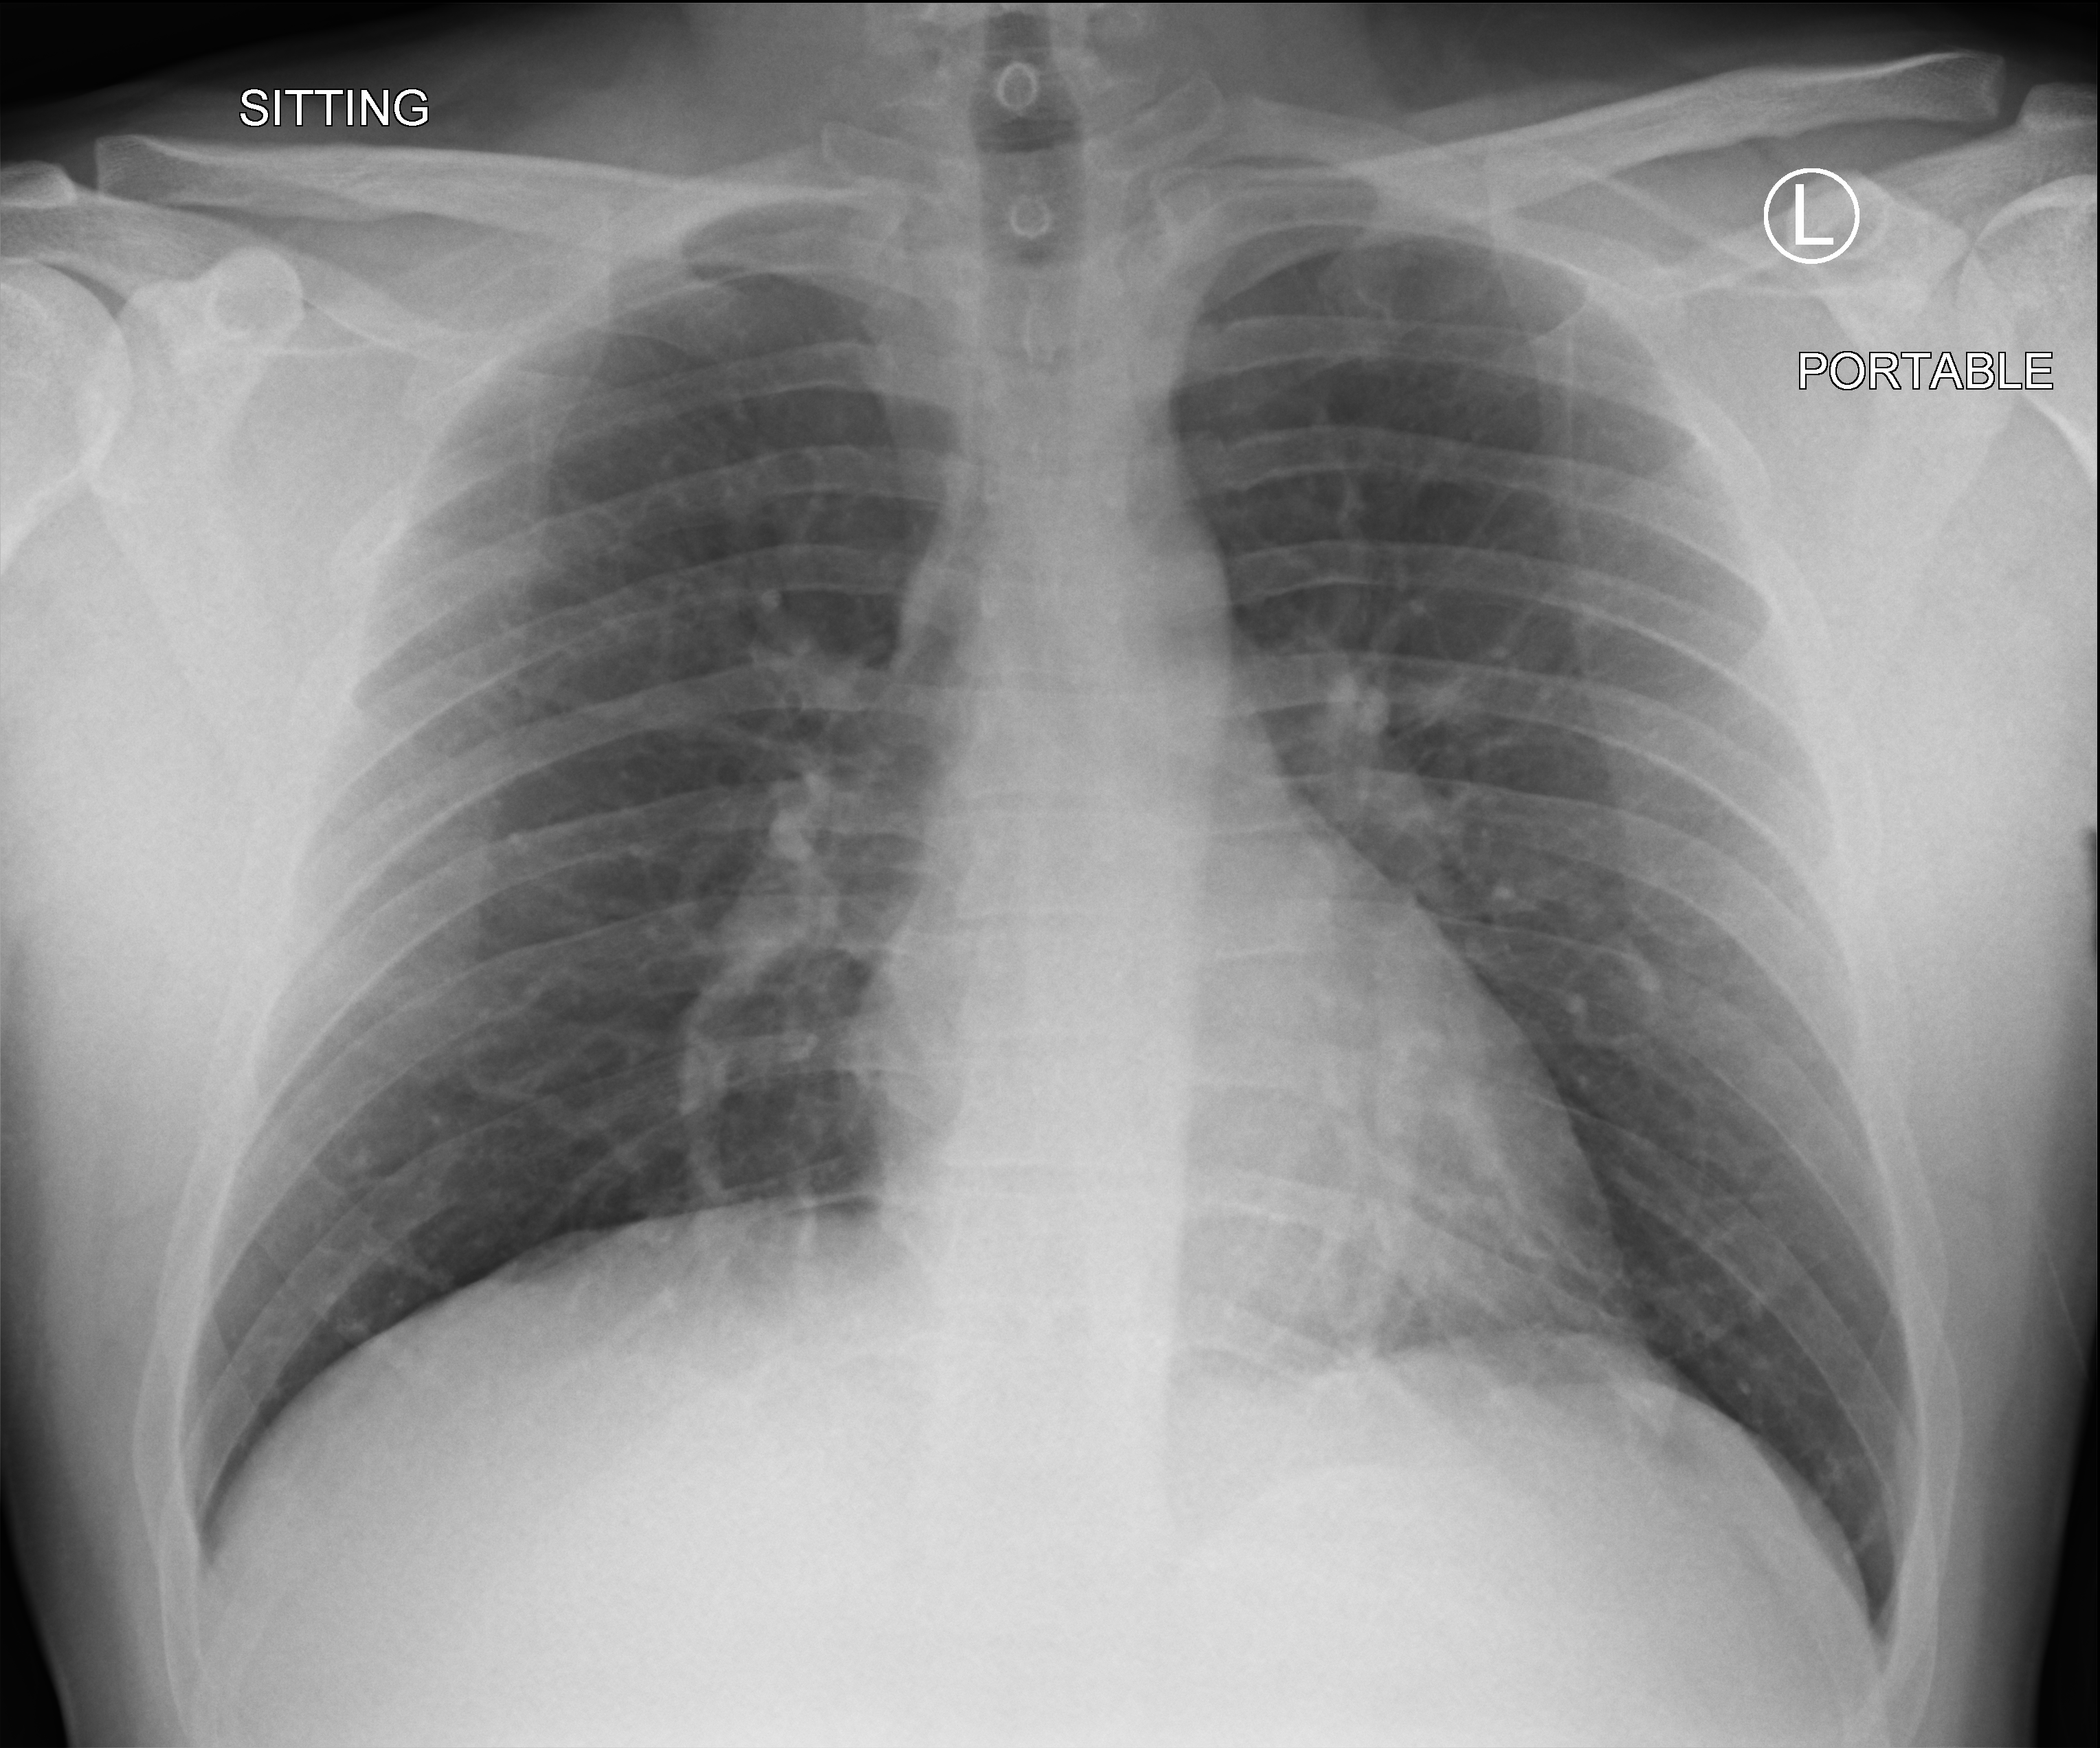
Chest X-ray (portable); anteroposterior (AP) projection. Patient hospitalised with COVID-19; male, aged 18–59 years.
Admission-level facts for this patient (not findings on this image; timing relative to this image not recorded): mechanically ventilated during this hospital stay: no; admitted to intensive care during this hospital stay: no.